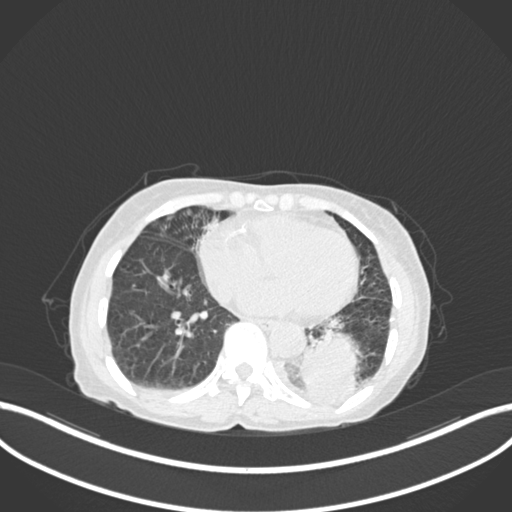
Chest CT, one axial slice. Slice 42 of 233 in the series (ordered by position). Reconstruction kernel B30f. 120 kVp. Lung window (W 1500 / L -600 HU). 1 mm slice thickness. 512 × 512 image matrix. Patient: female, 78 years. Case-level facts recorded for this patient, not image findings: clinical TNM (as recorded): T3 N0 M1.
Outlined on this slice (bounding box drawn by a radiologist):
- lung tumour (recorded histology: squamous cell carcinoma): bounding box (x1, y1, x2, y2) in pixels: (299, 325, 362, 407)